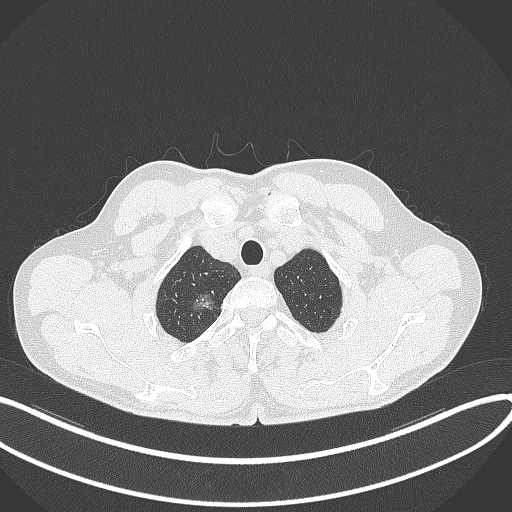
Chest CT, one axial slice; slice 345 of 407 in the series (ordered by position); reconstruction kernel B70f; lung window (W 1500 / L -600 HU); 512 × 512 image matrix, field of view 400 × 400 mm. Male patient, age 58 years. Case-level facts recorded for this patient, not image findings: clinical TNM (as recorded): T1c N0 M0.
Outlined on this slice (rectangle marked by the reading radiologist):
- lung tumour (recorded histology: adenocarcinoma): box from (x=190, y=289) to (x=223, y=322) px